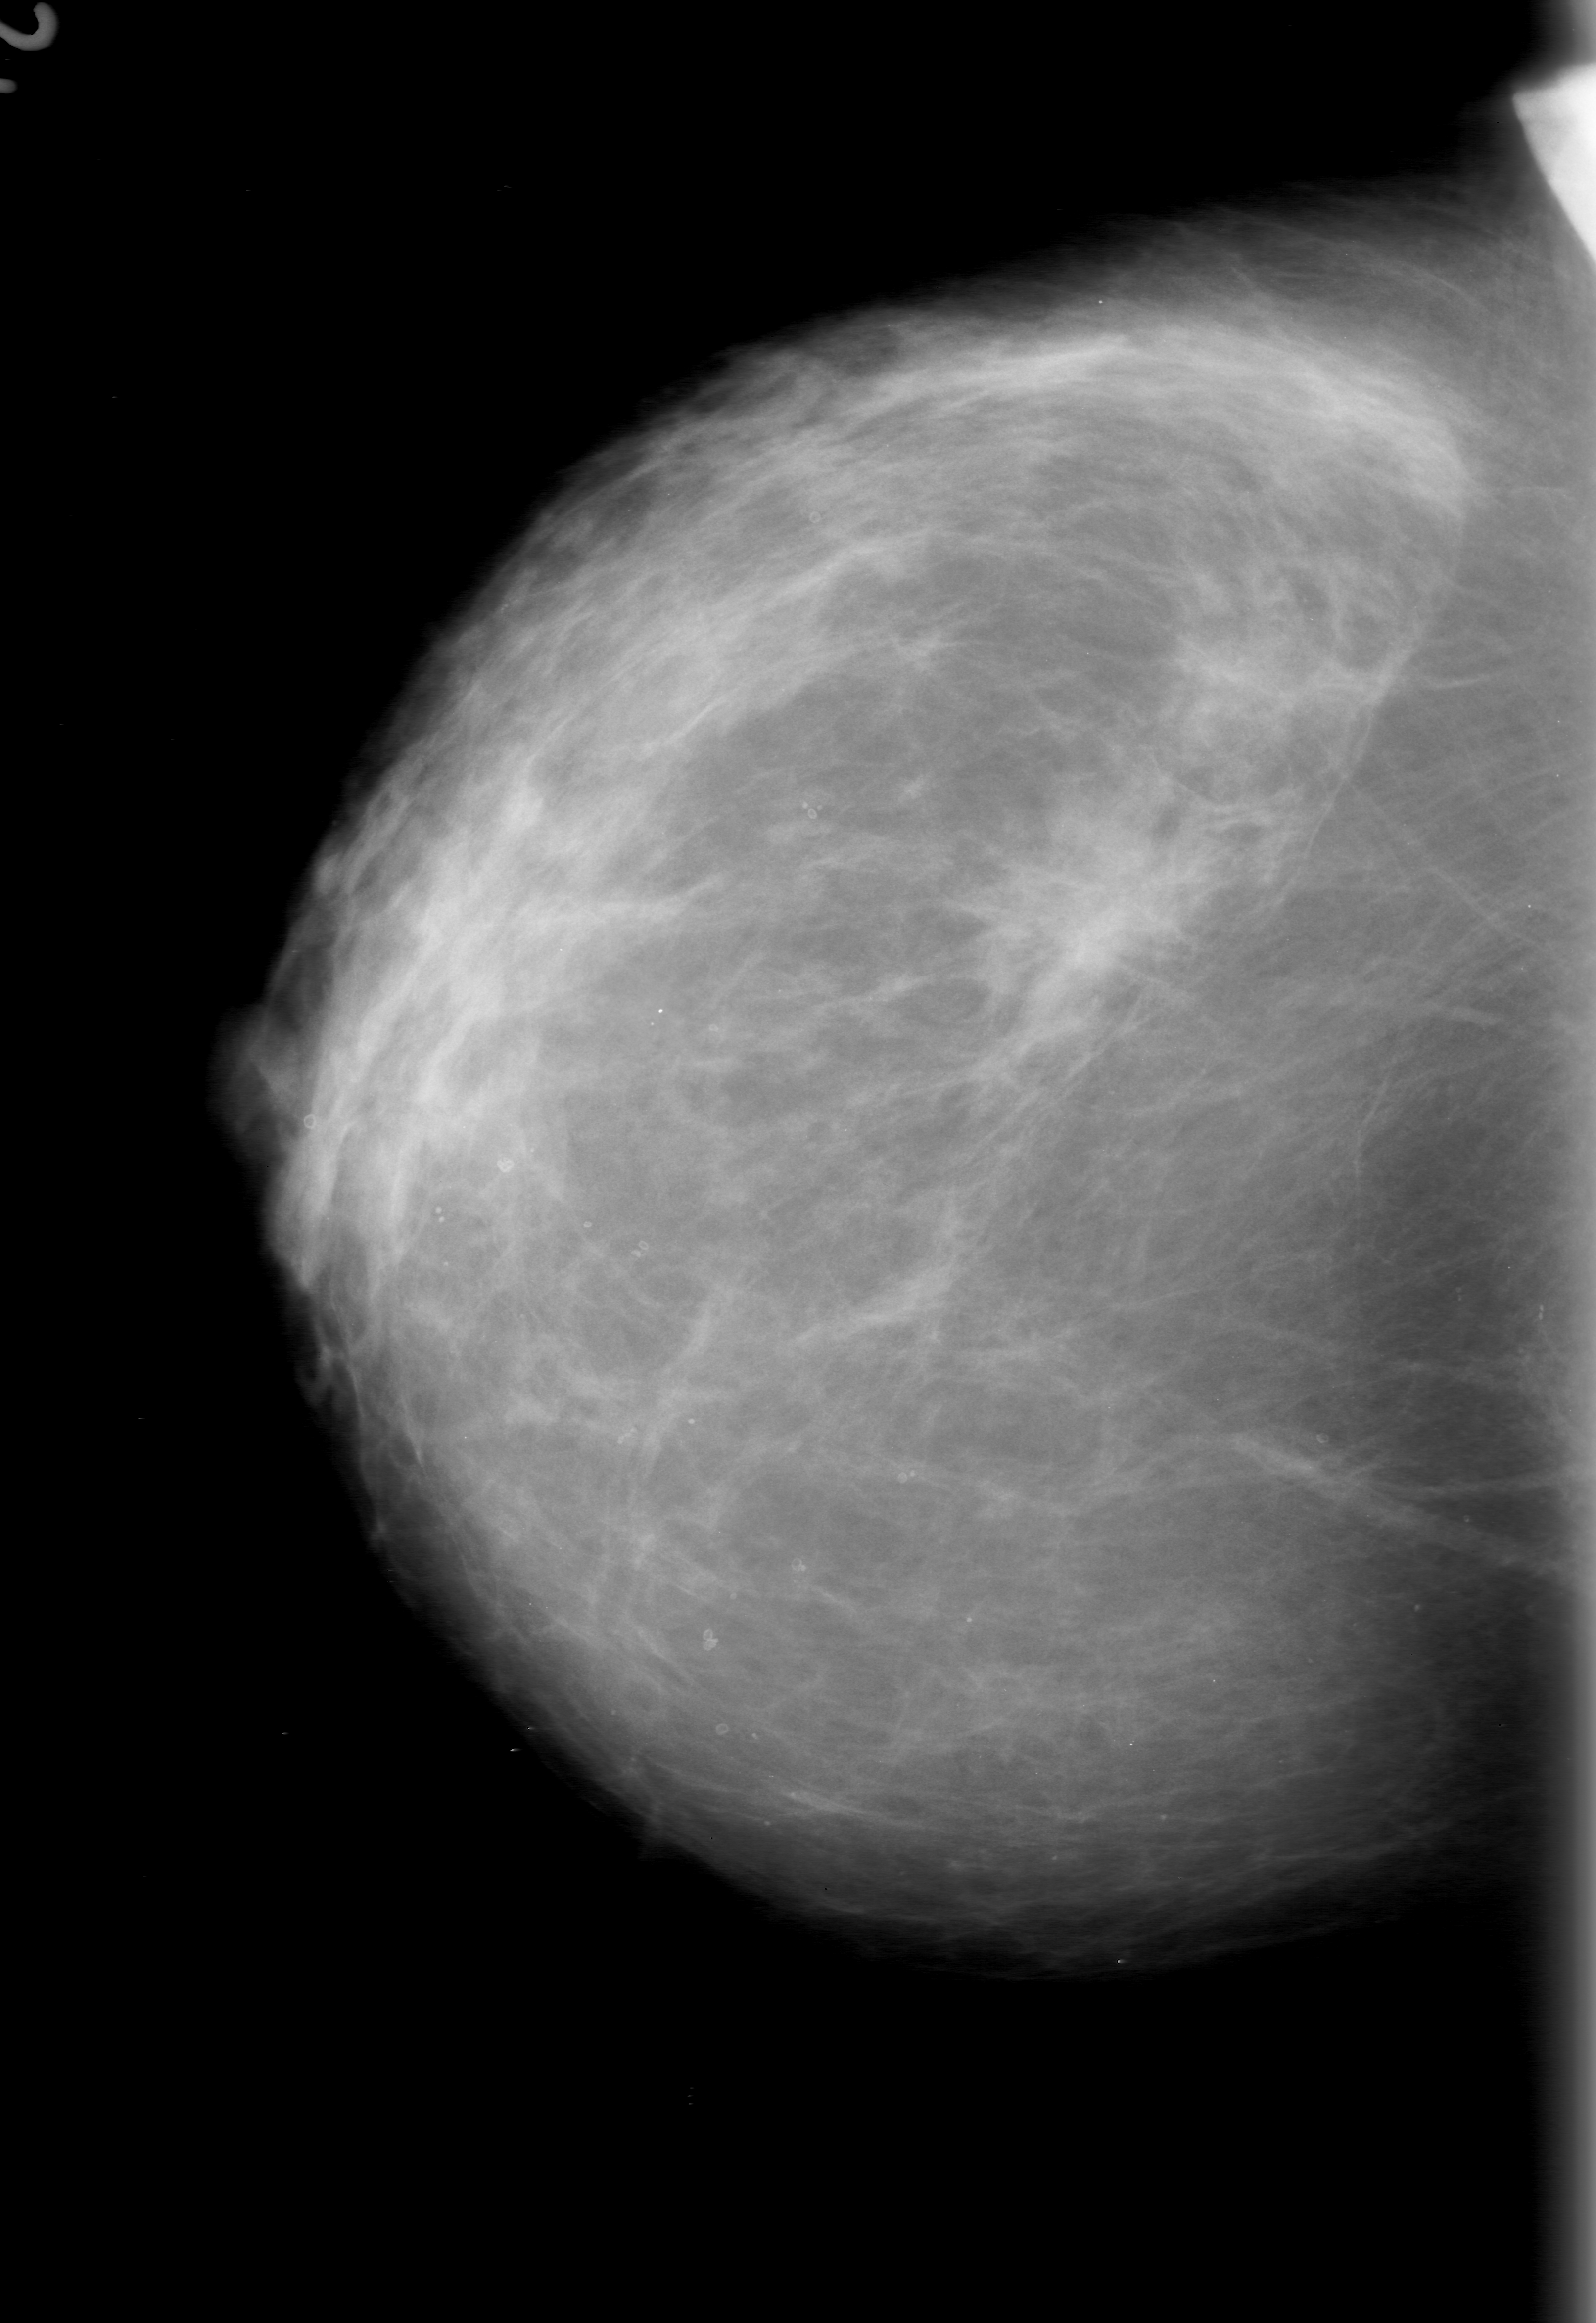
Digitized screen-film mammogram. Right breast. Craniocaudal (CC) view. BI-RADS breast density category 2 (scale 1–4). 1596 × 2323 image matrix.
Marked abnormalities (boxes around the expert regions of interest):
- mass, shape architectural distortion; BI-RADS assessment category 0 (incomplete: needs additional imaging); subtlety rating 4 on a 1 (subtle) to 5 (obvious) scale; pathology result (as recorded, not read from the image): malignant: box from (x=929, y=797) to (x=1223, y=1085) px